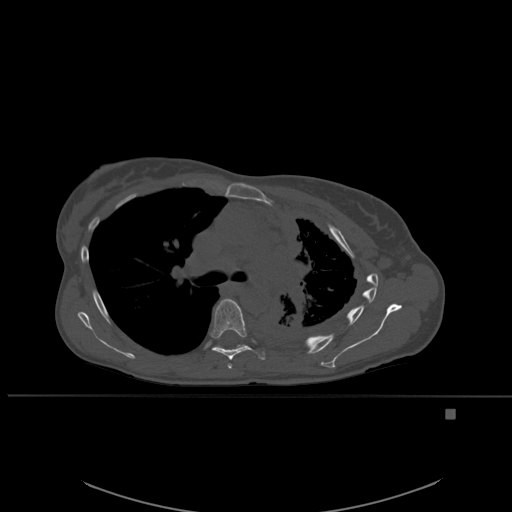
CT including the spine, one axial slice; slice 382 of 537 in the series (ordered by position); bone window (W 1800 / L 400 HU); 1.5 mm slice thickness; 512 × 512 image matrix, field of view 440 × 440 mm. Female patient, age 45 years. Case-level facts recorded for this patient, not image findings: primary cancer: lung.
Annotated regions visible in this slice (semi-automatic segmentation, software-assisted and operator-edited):
- T5 vertebra: bounding box <228,364,232,369> (left, top, right, bottom; pixels)
- T6 vertebra: <210,299,265,361>
- T7 vertebra: <215,344,245,348>